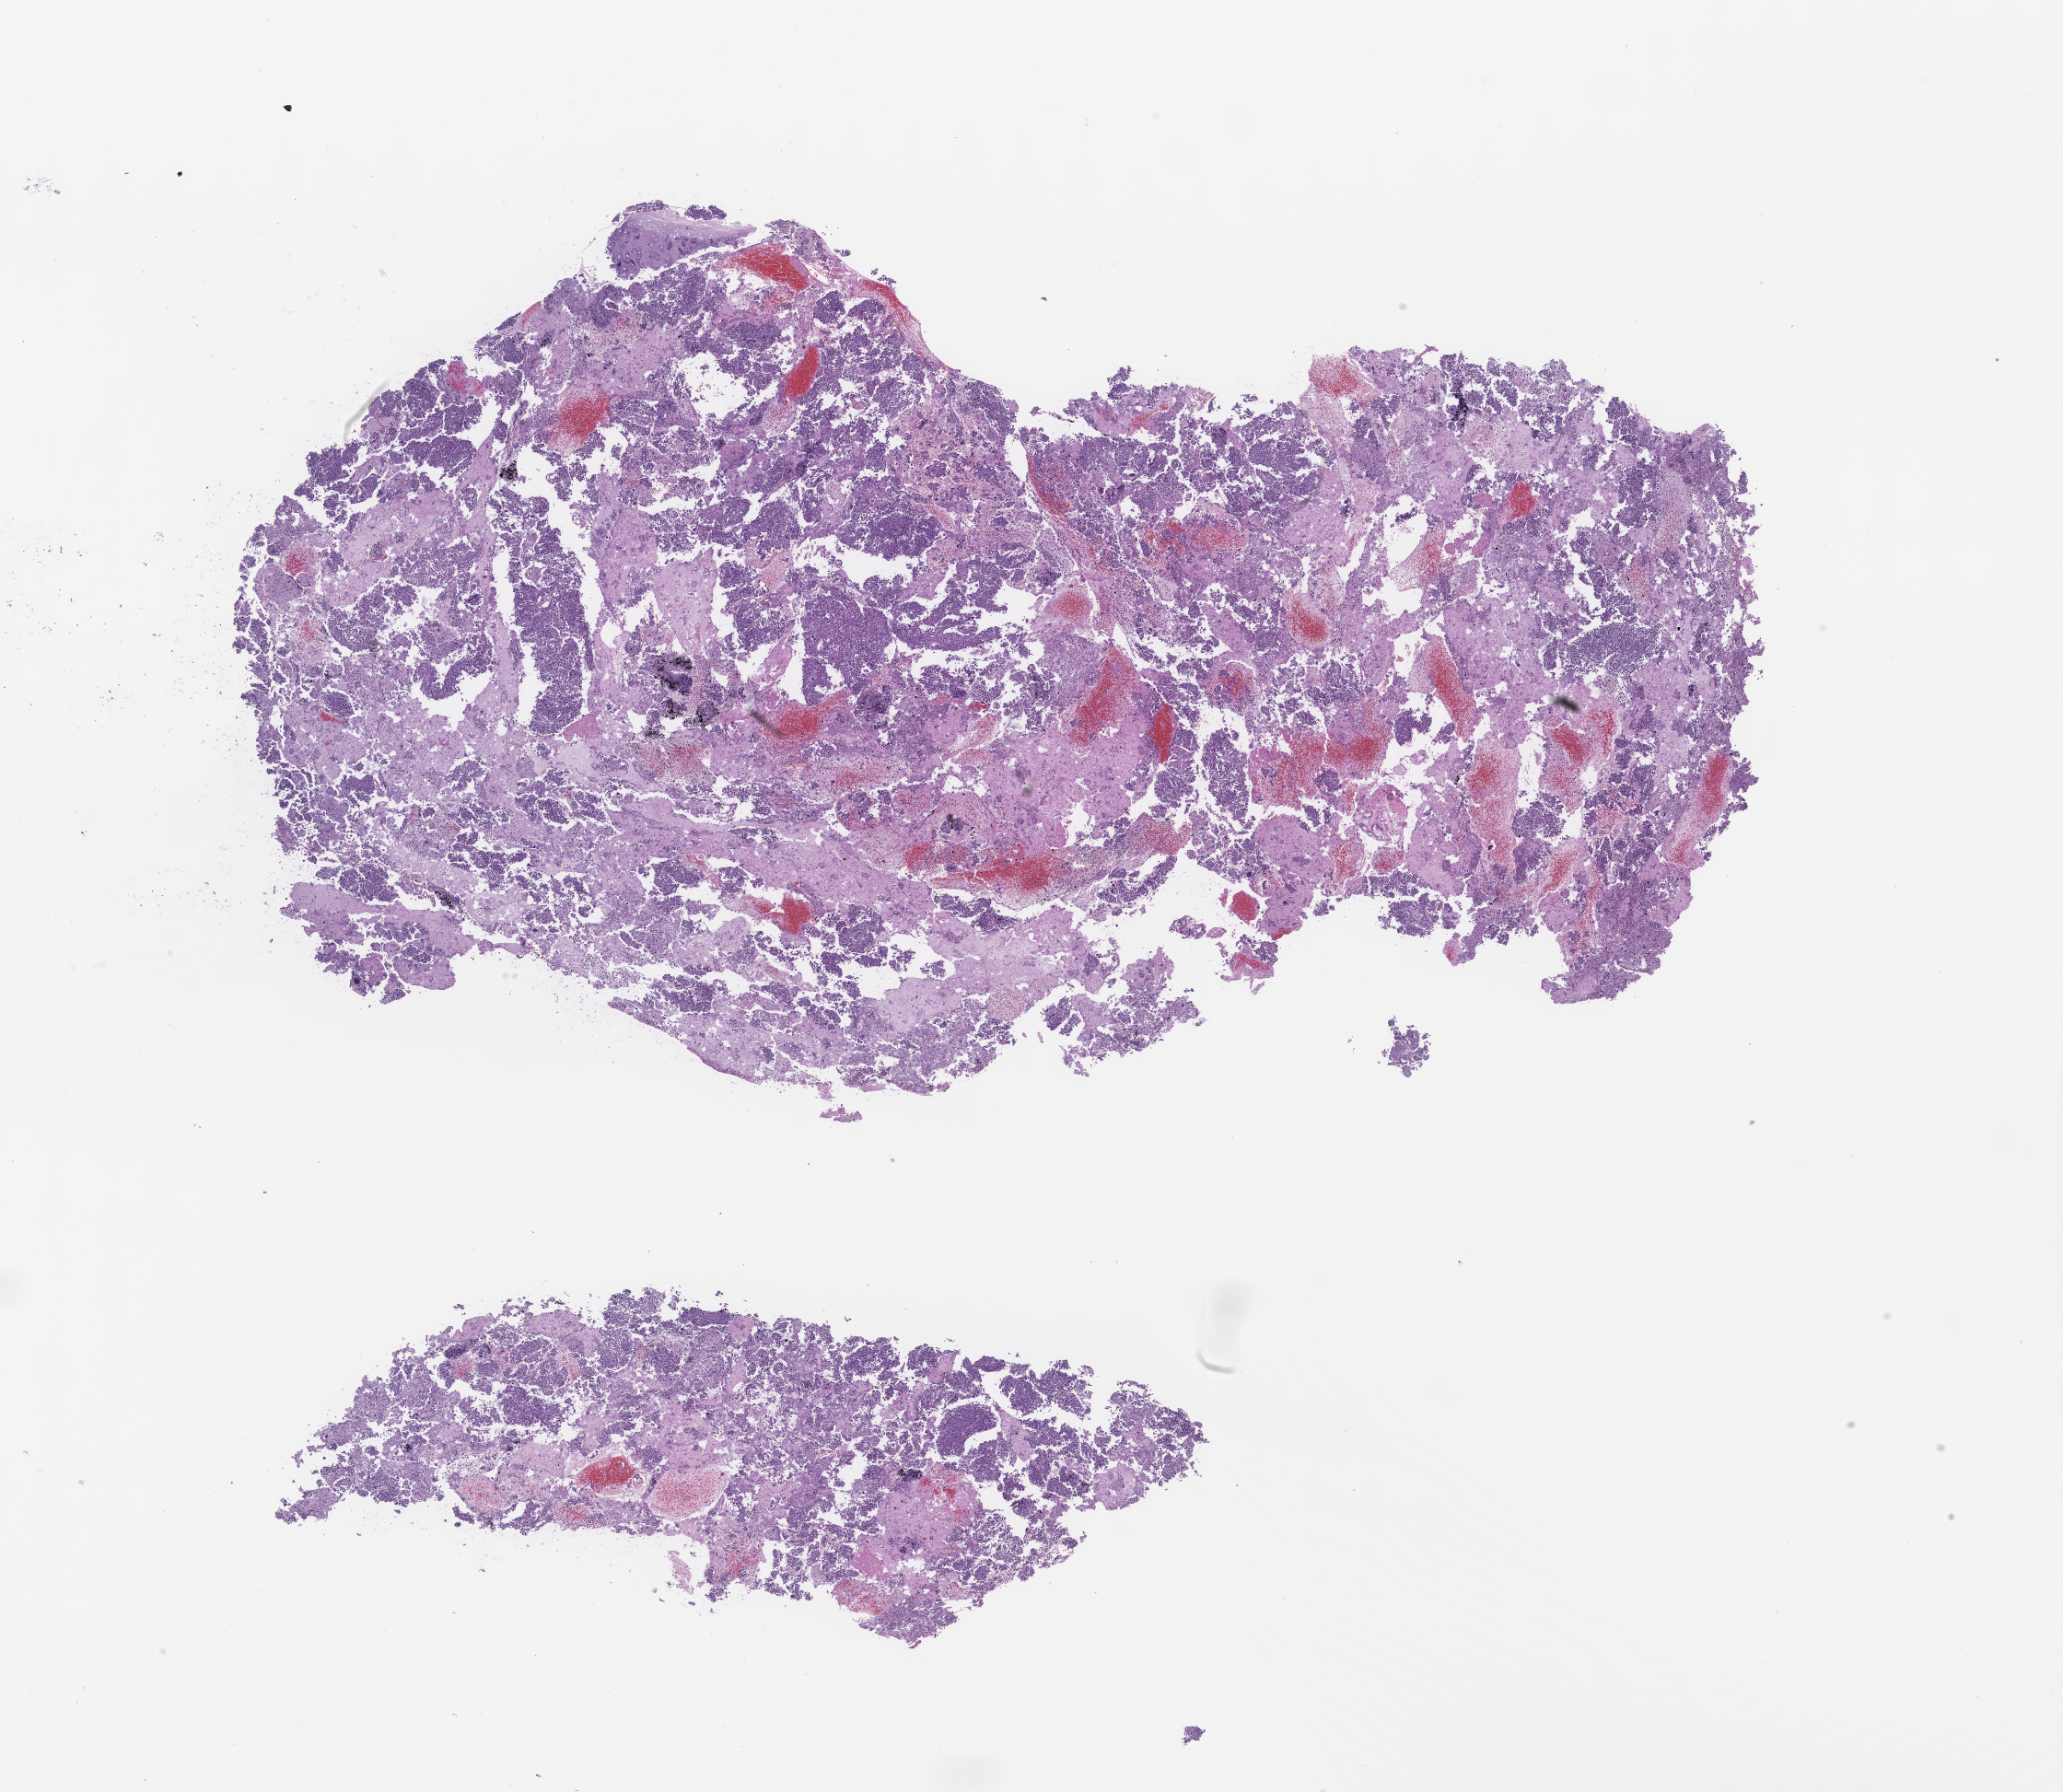
Haematoxylin and eosin whole-slide image — whole scanned area (about 18.1 x 15.7 mm) shown as a low-resolution overview. FFPE section. Patient: female.
This section: metastatic tumor tissue. Primary diagnosis of the patient: Non-Small Cell Lung Carcinoma.